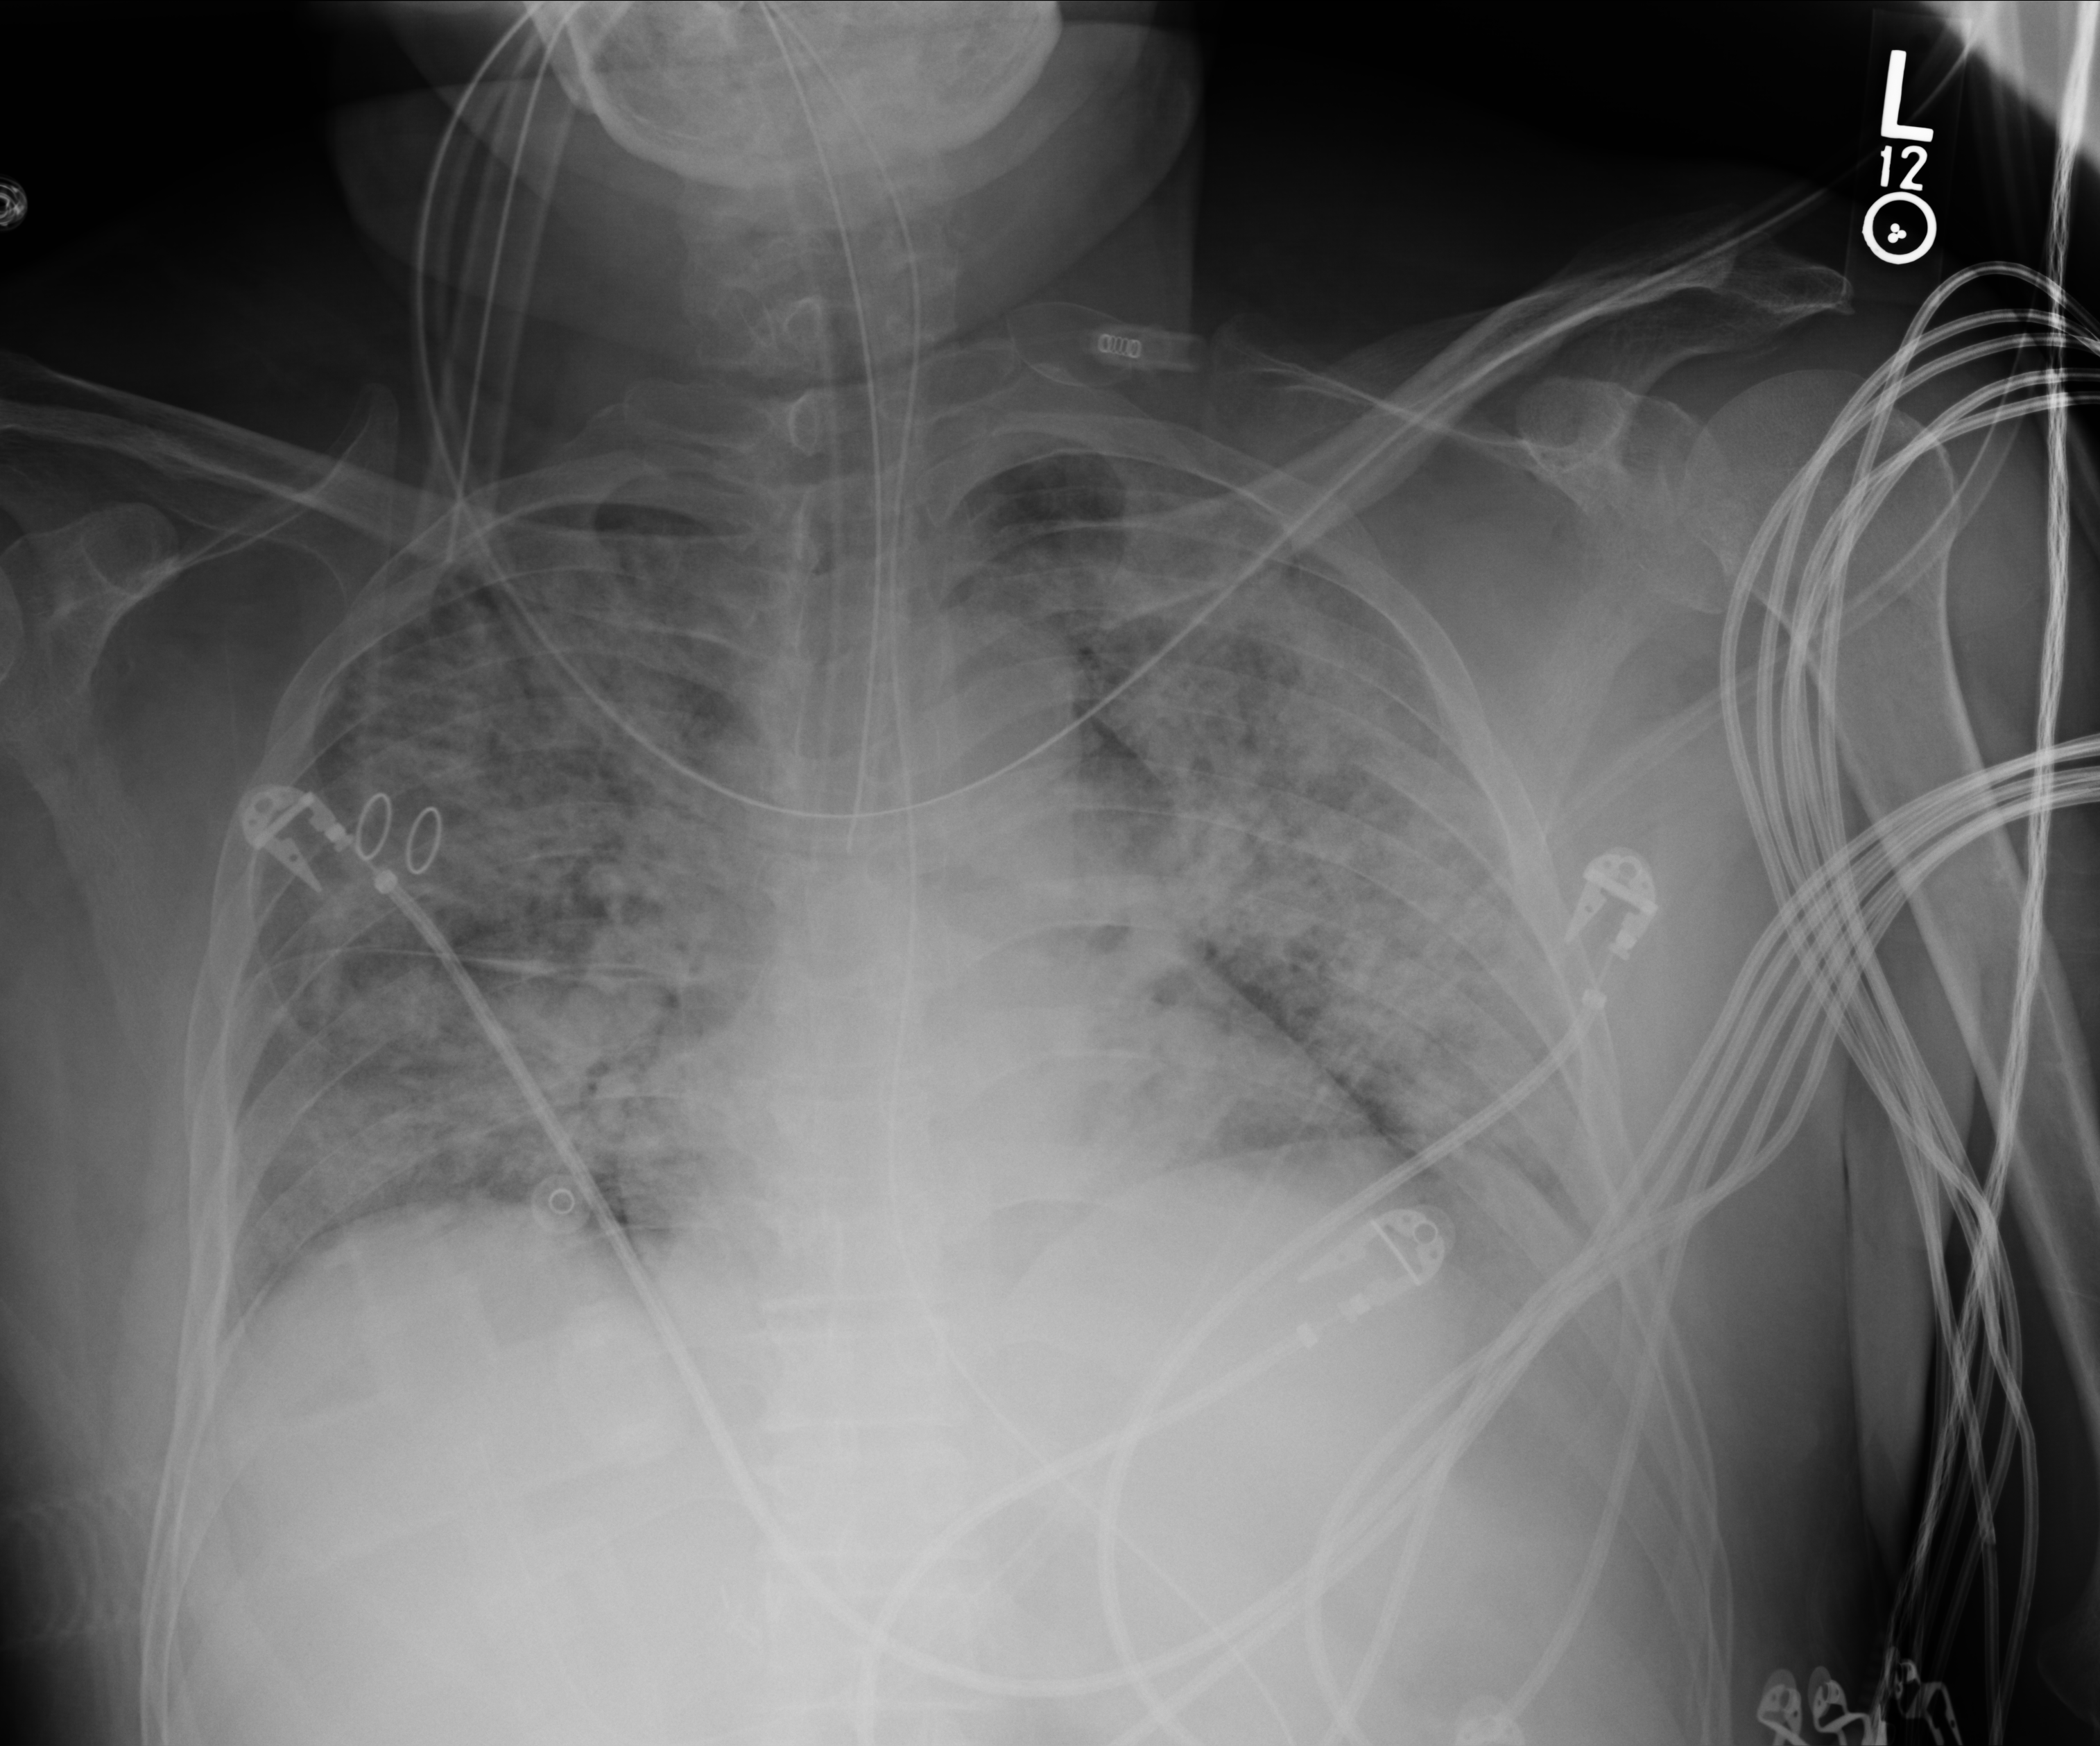
Chest X-ray (portable). Patient hospitalised with COVID-19; male, aged 60–74 years.
From the hospital-stay record, not from the radiograph (when in the stay this image was taken is not recorded):
- COPD (admission record): no